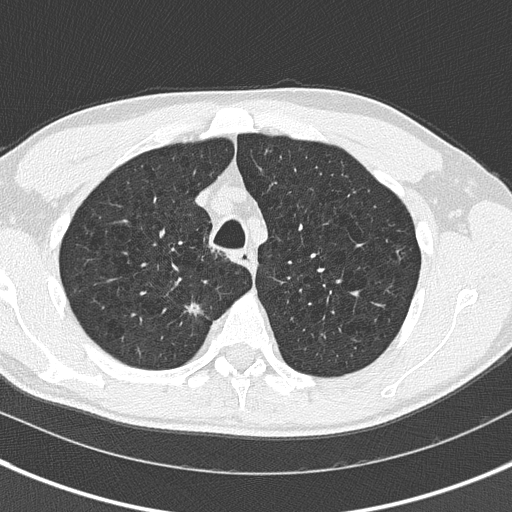
Low-dose screening chest CT, axial slice. First (baseline) screen. Lung window (W 1500 / L -600 HU). Lung (sharp) reconstruction kernel (B50f). 120 kVp. Slice 40 of 175 in the series. 512 × 512 image matrix. Male participant, aged 56 years at enrolment. Current smoker at enrolment.
Expert reader's lesion annotation, bounding box (x1, y1, x2, y2) in pixels: (177, 293, 223, 335). The screening reader recorded 3 non-calcified nodules or masses ≥4 mm on this exam (right upper lobe, right upper lobe, left lower lobe); which of them this box marks is not recorded. Later outcome: lung cancer diagnosed 228 days after this screen — non-small cell carcinoma, right upper lobe, stage IIIA (AJCC 6th edition), 21 mm at pathology.